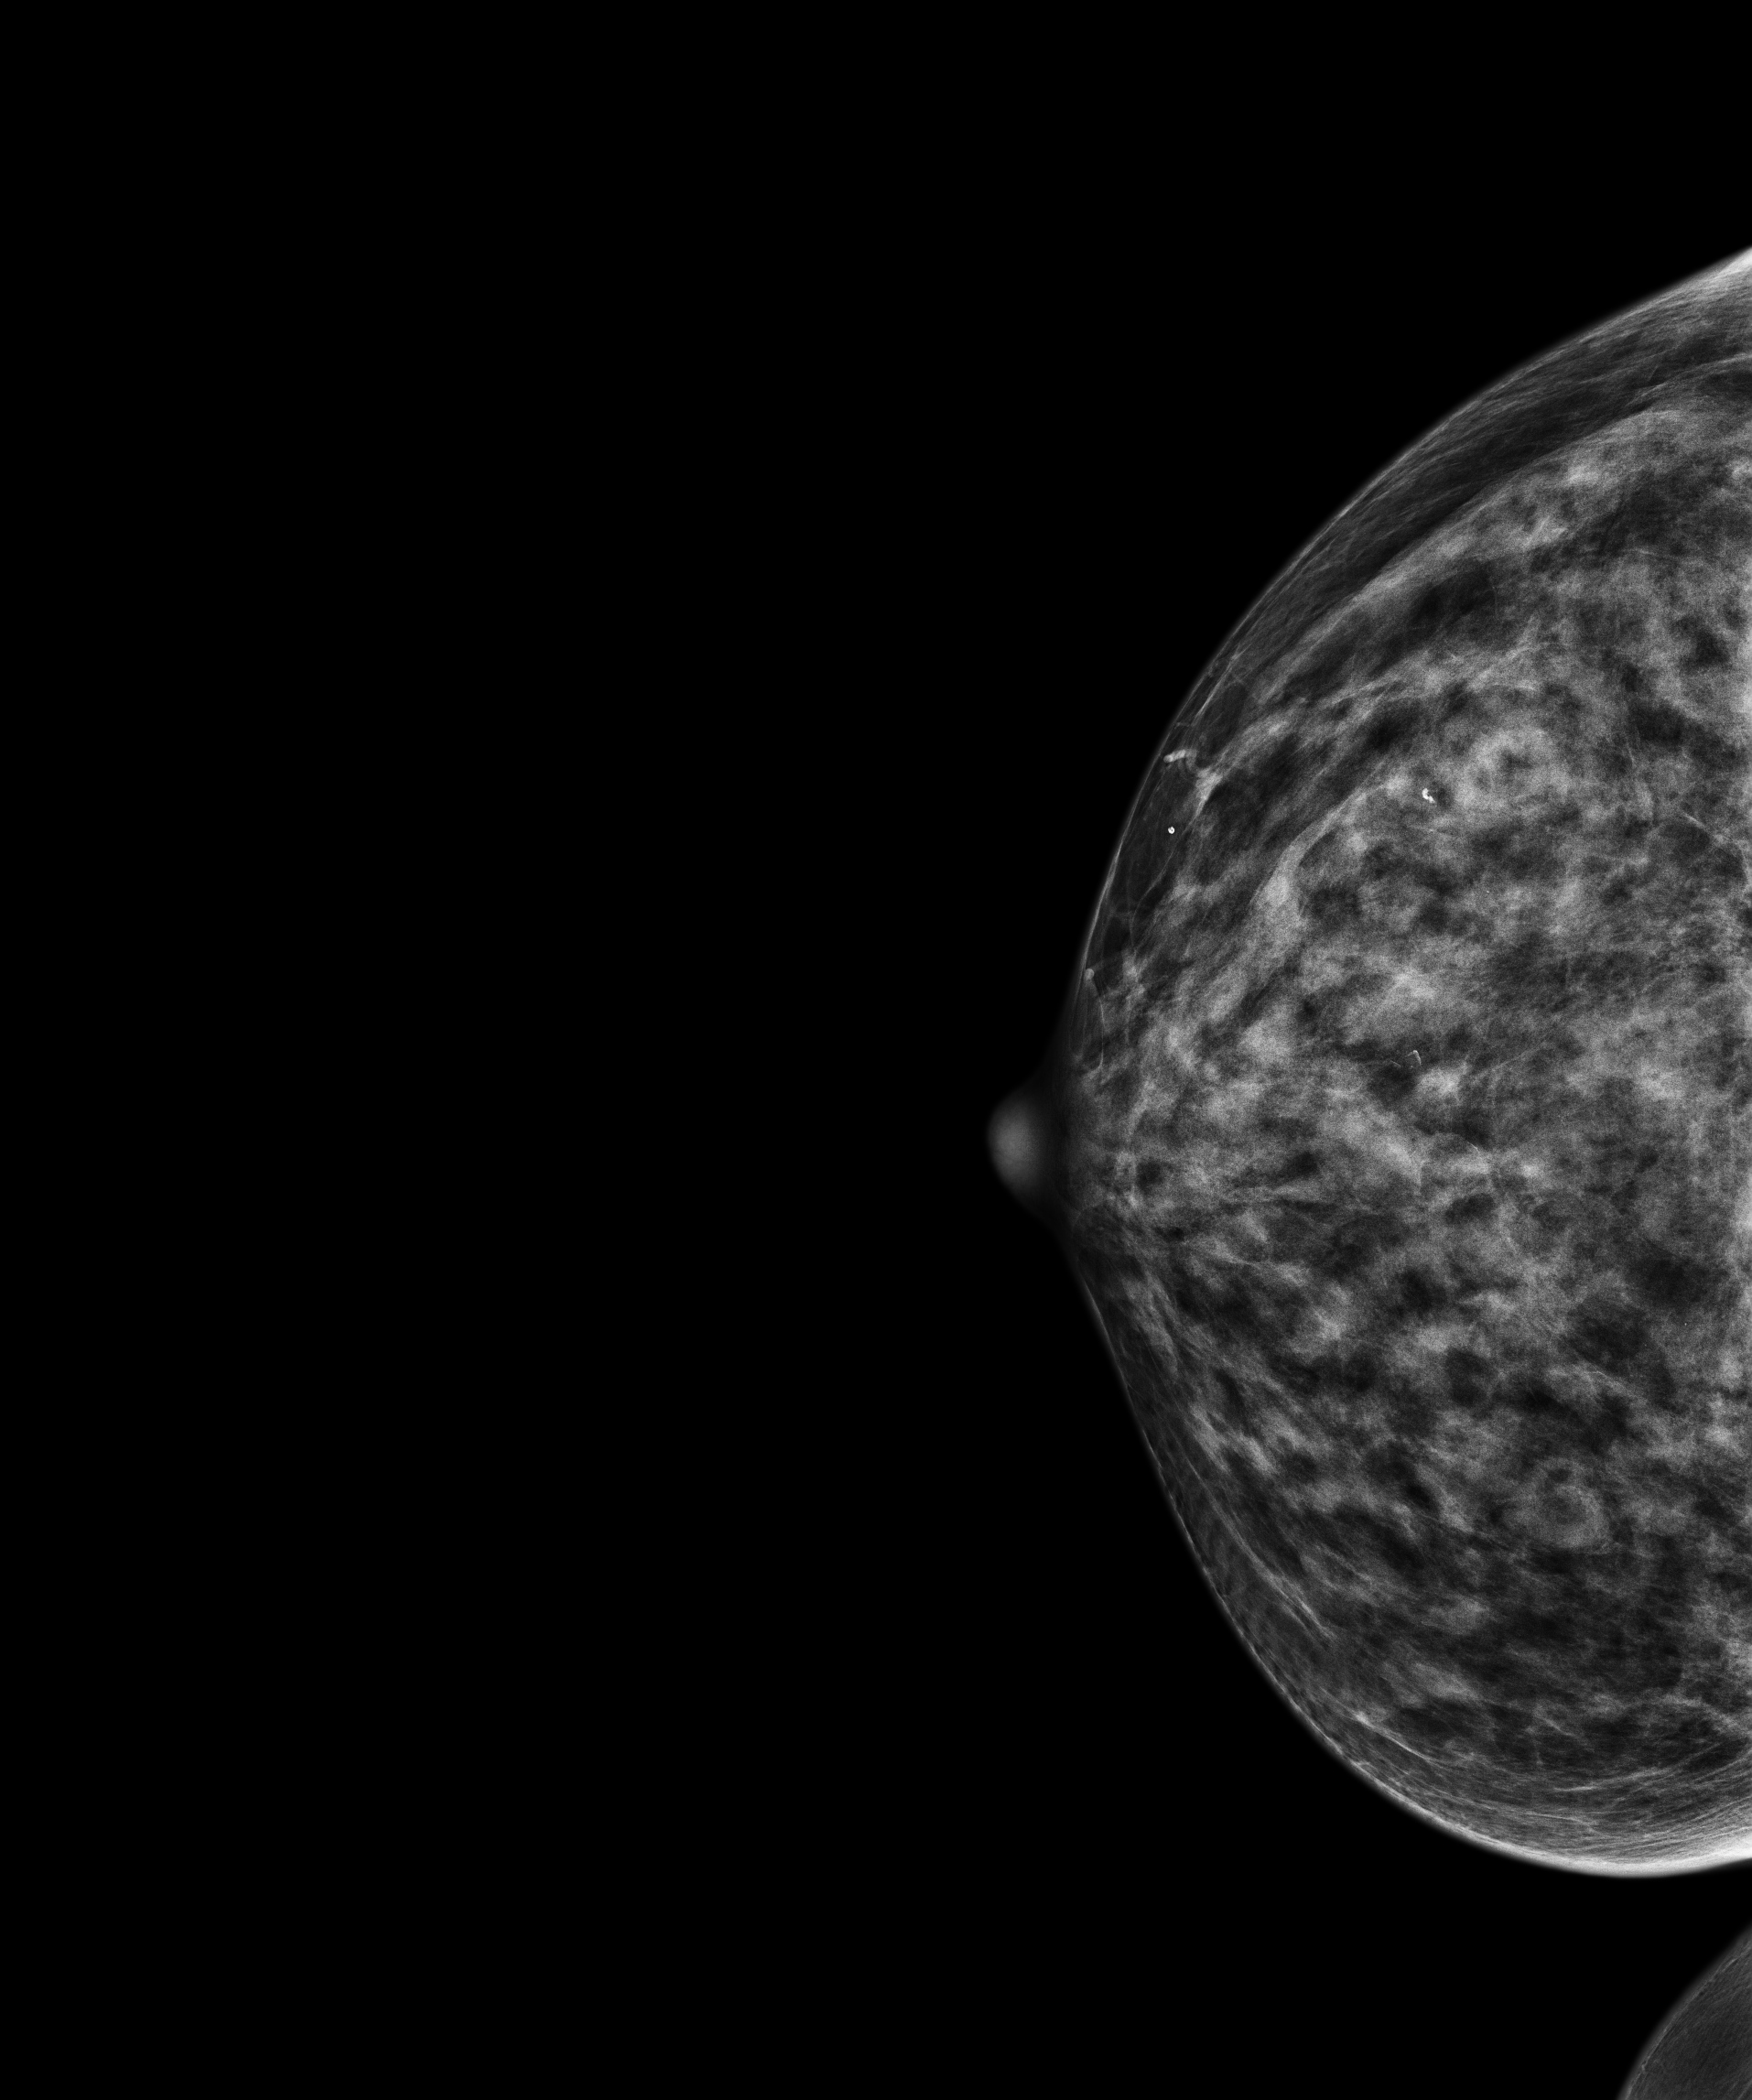
Full-field digital mammogram (FFDM); right breast; CC view; annual screening mammography examination; compressed breast thickness 42.4 mm; system: Senographe Pristina. Patient aged 73 years (female).
Breast density at the screening exam (both breasts): extremely dense (BI-RADS density category d). Final BI-RADS category for the screening round (tomosynthesis exam, both breasts): category 1. Recall: no recall after this screen.